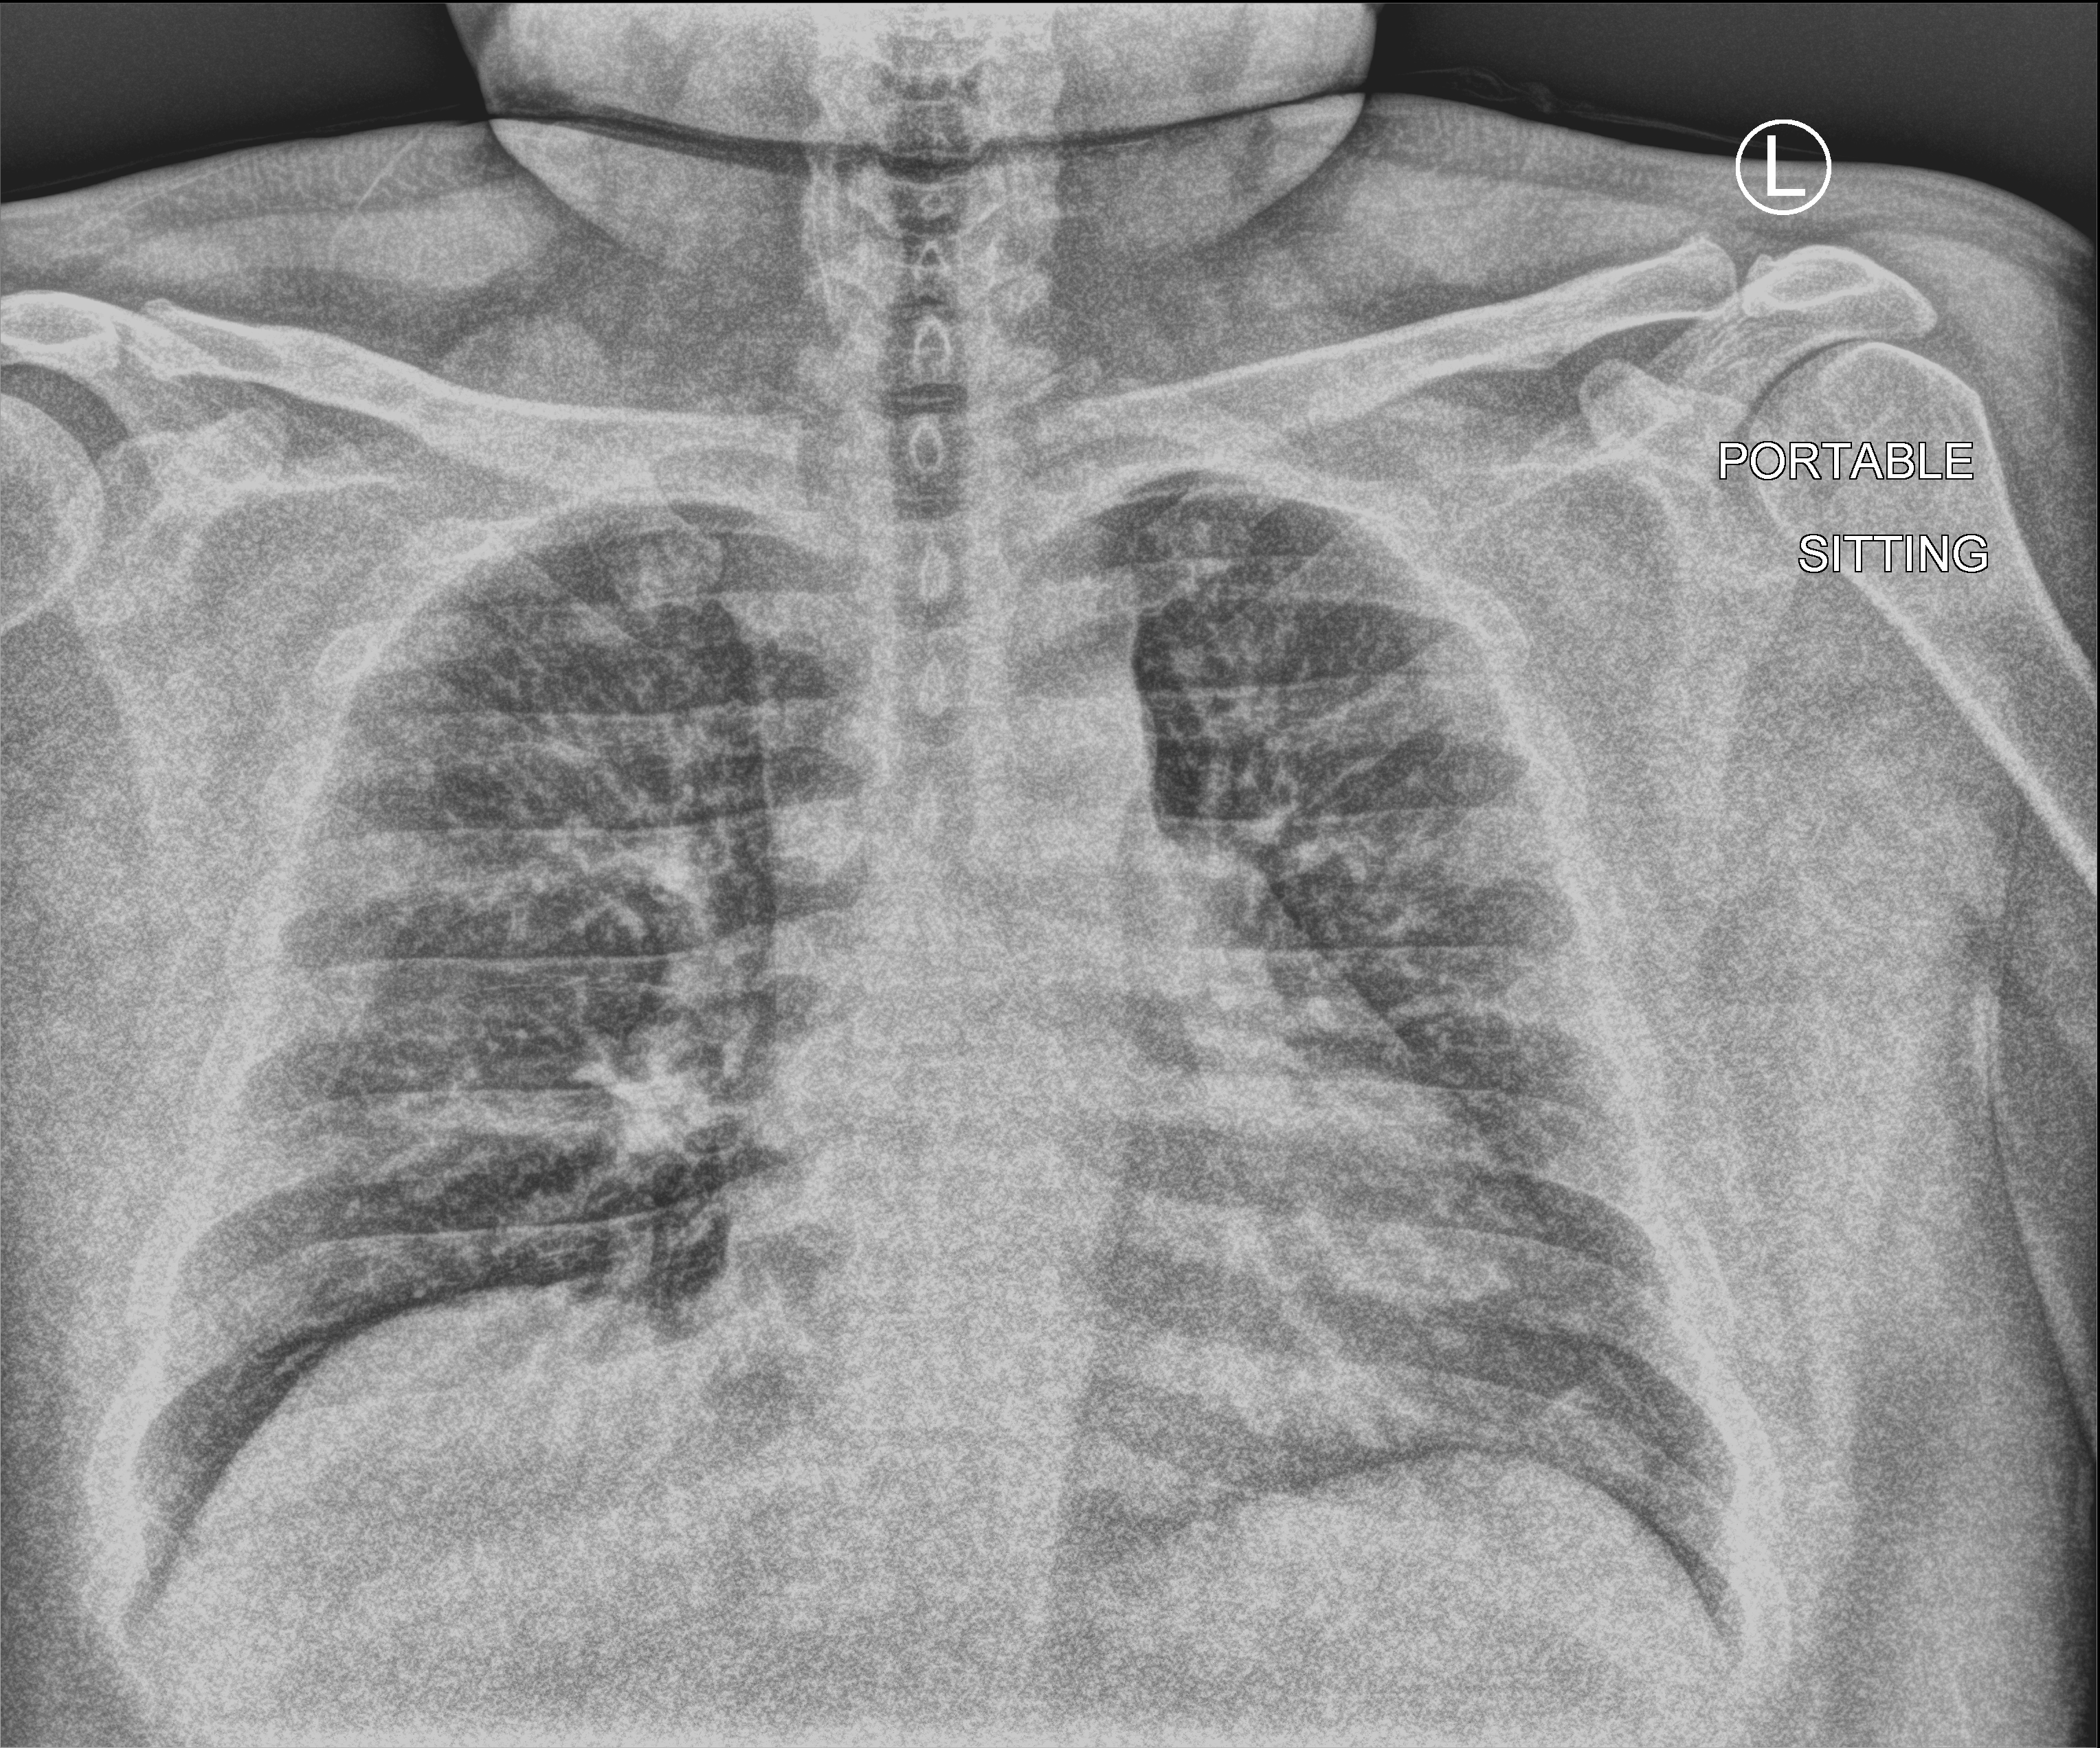
Portable chest radiograph; anteroposterior (AP) projection. Adult patient hospitalised with COVID-19, age 18–59 years.
Hospital-stay facts (about this admission, not read from this image; timing relative to this image not recorded): admitted to intensive care during this hospital stay: yes.